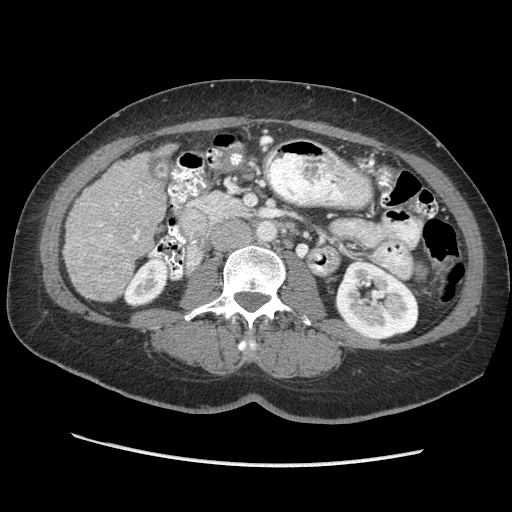
Contrast-enhanced abdominal CT (liver protocol), one axial slice. Slice 100 of 170 in the series (ordered by position). Soft-tissue window (W 400 / L 40 HU). 2.5 mm slice thickness. 512 × 512 image matrix, field of view 360 × 360 mm. Case-level facts recorded for this patient, not image findings: diagnosis: hepatocellular carcinoma (patient treated with transarterial chemoembolisation; whether this scan precedes or follows treatment is not stated here); TNM stage (as recorded): Stage-II; Child-Pugh class: A; tumour differentiation: no biopsy.
Structures marked on this image (semi-automatic segmentation, software-assisted and operator-edited):
- liver parenchyma outside the tumour (the mass and vessels are separate outlines, so this box may not span the whole liver): bounding box (x1, y1, x2, y2) in pixels: (62, 144, 175, 300)
- liver vessels: (99, 190, 142, 241)